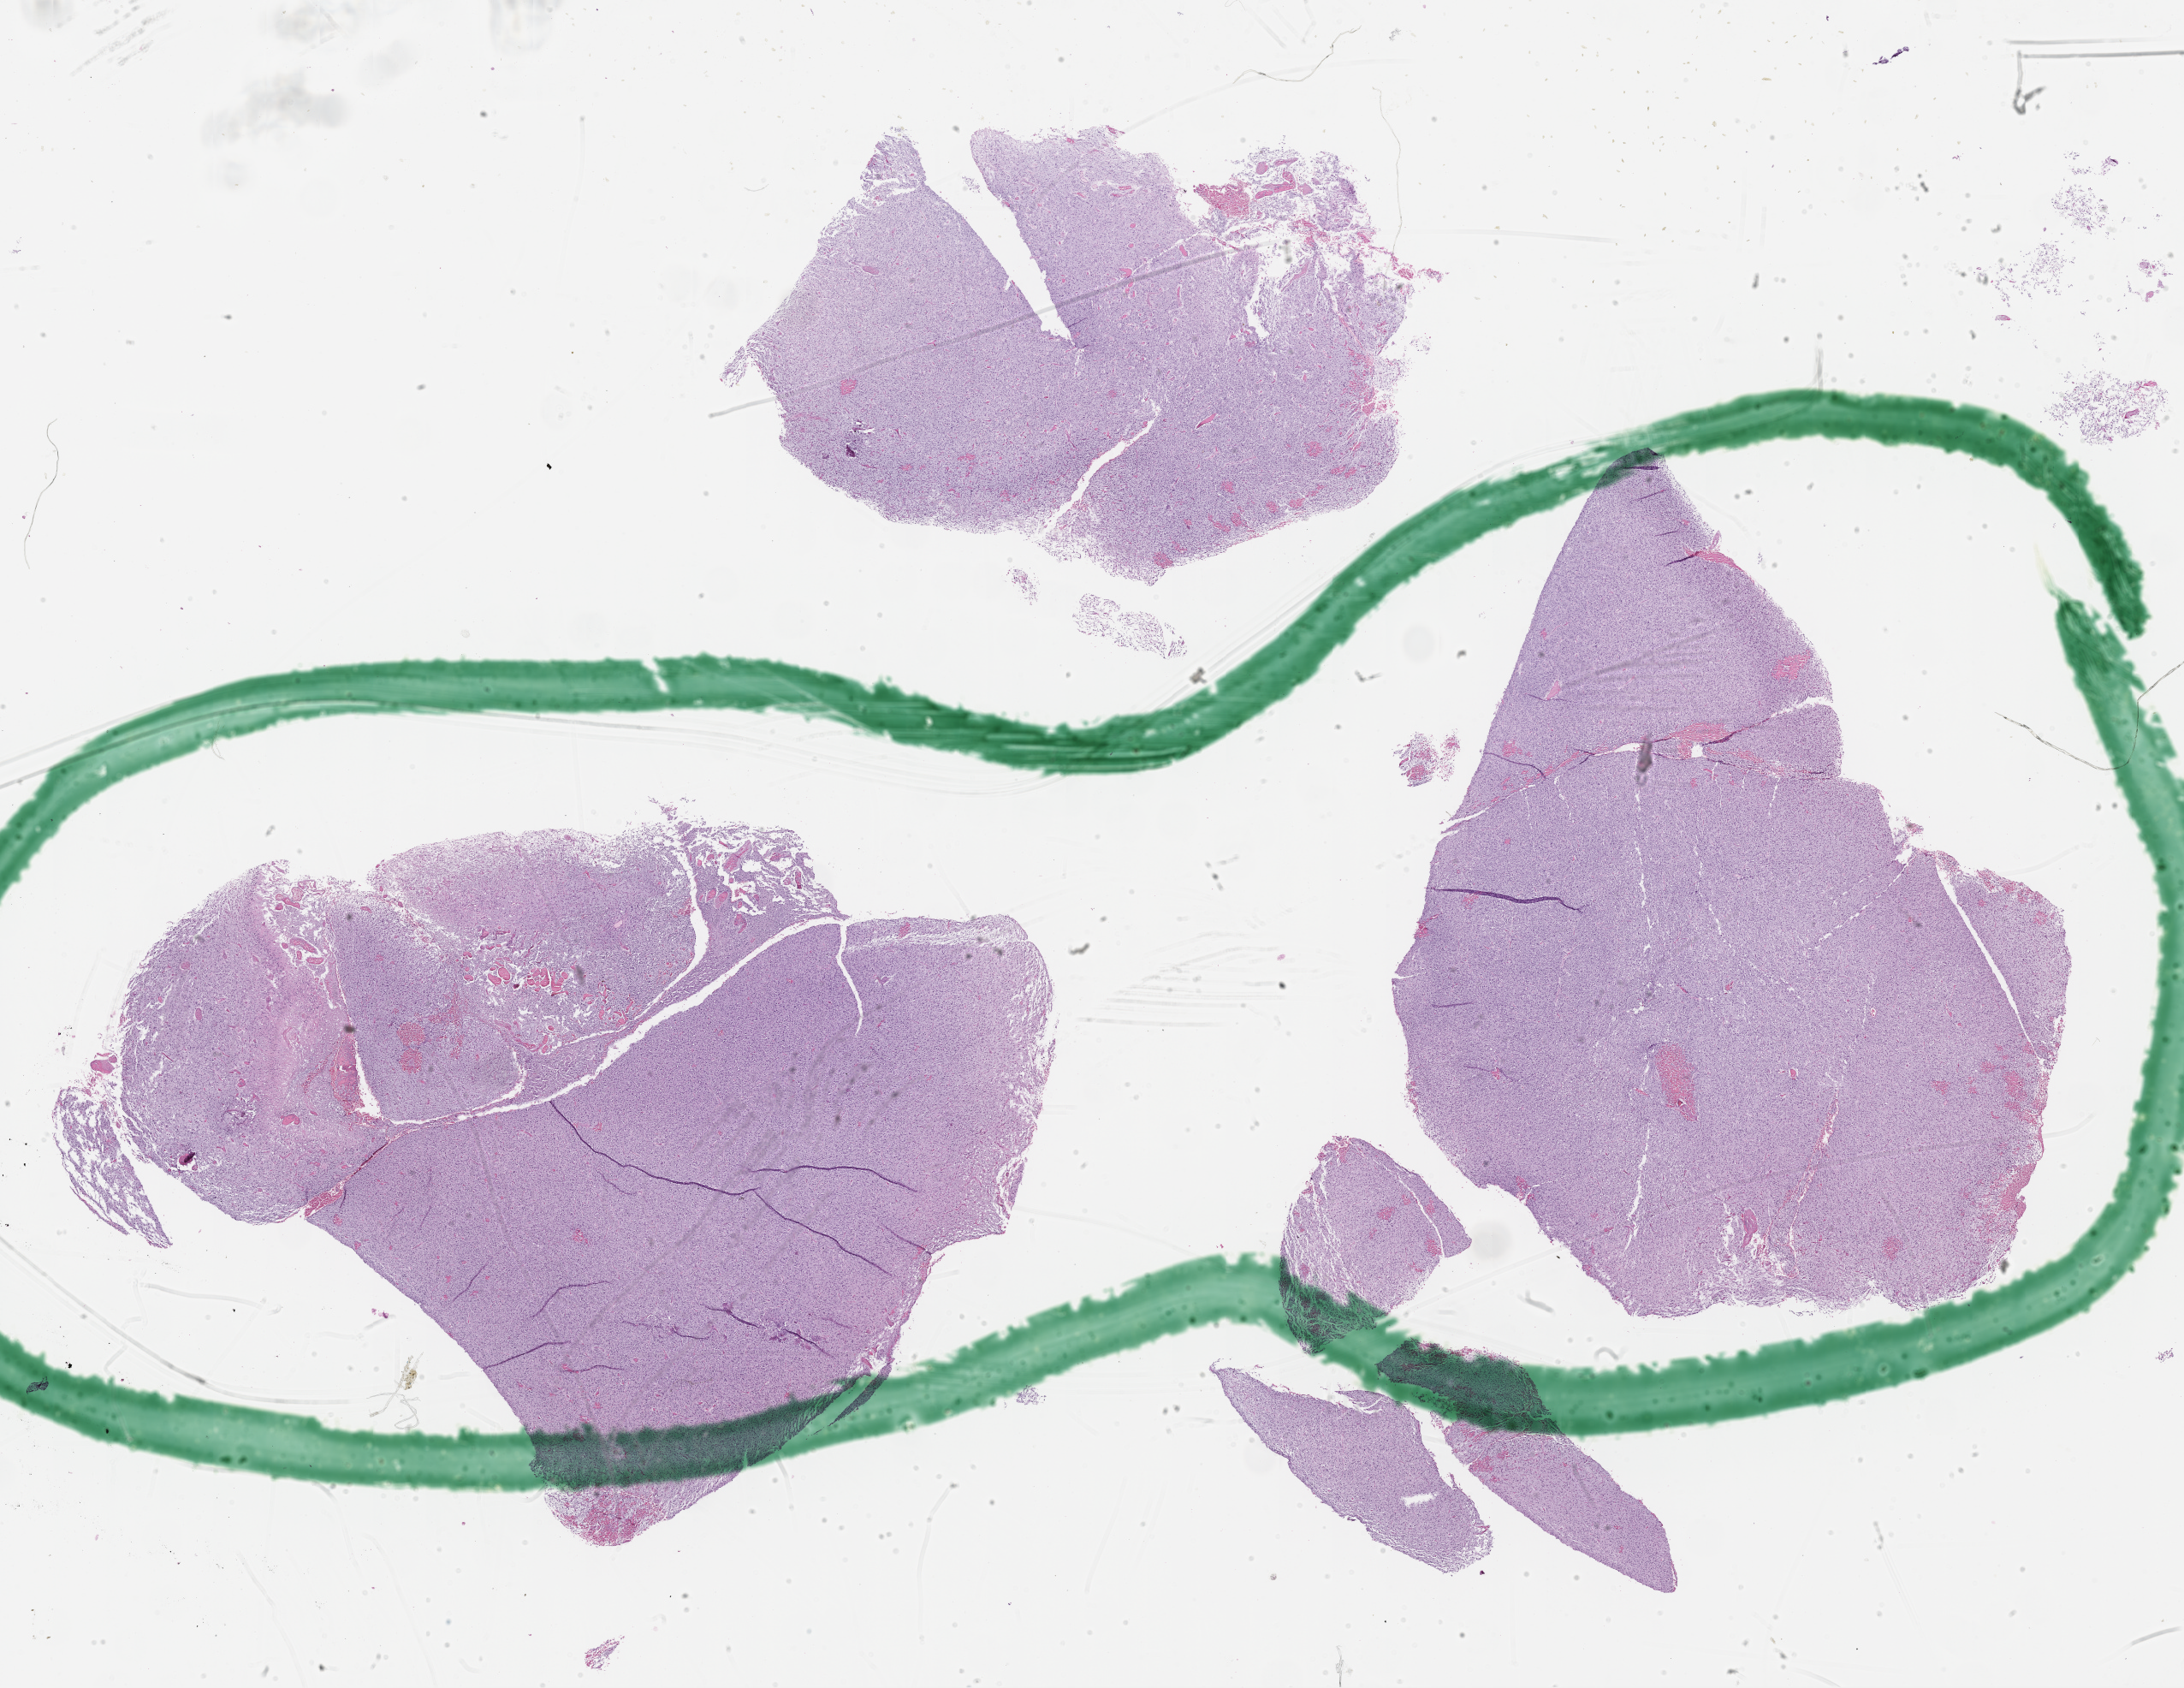
Hematoxylin and eosin (H&E) stained whole-slide image, shown as a low-resolution overview of the whole scanned area (about 20.7 x 16.0 mm, slide scanned at 40x); formalin-fixed paraffin-embedded (FFPE) diagnostic section; primary tumour sample from the brain. Female patient; age at initial diagnosis 18 years.
• pathologic diagnosis: Glioblastoma